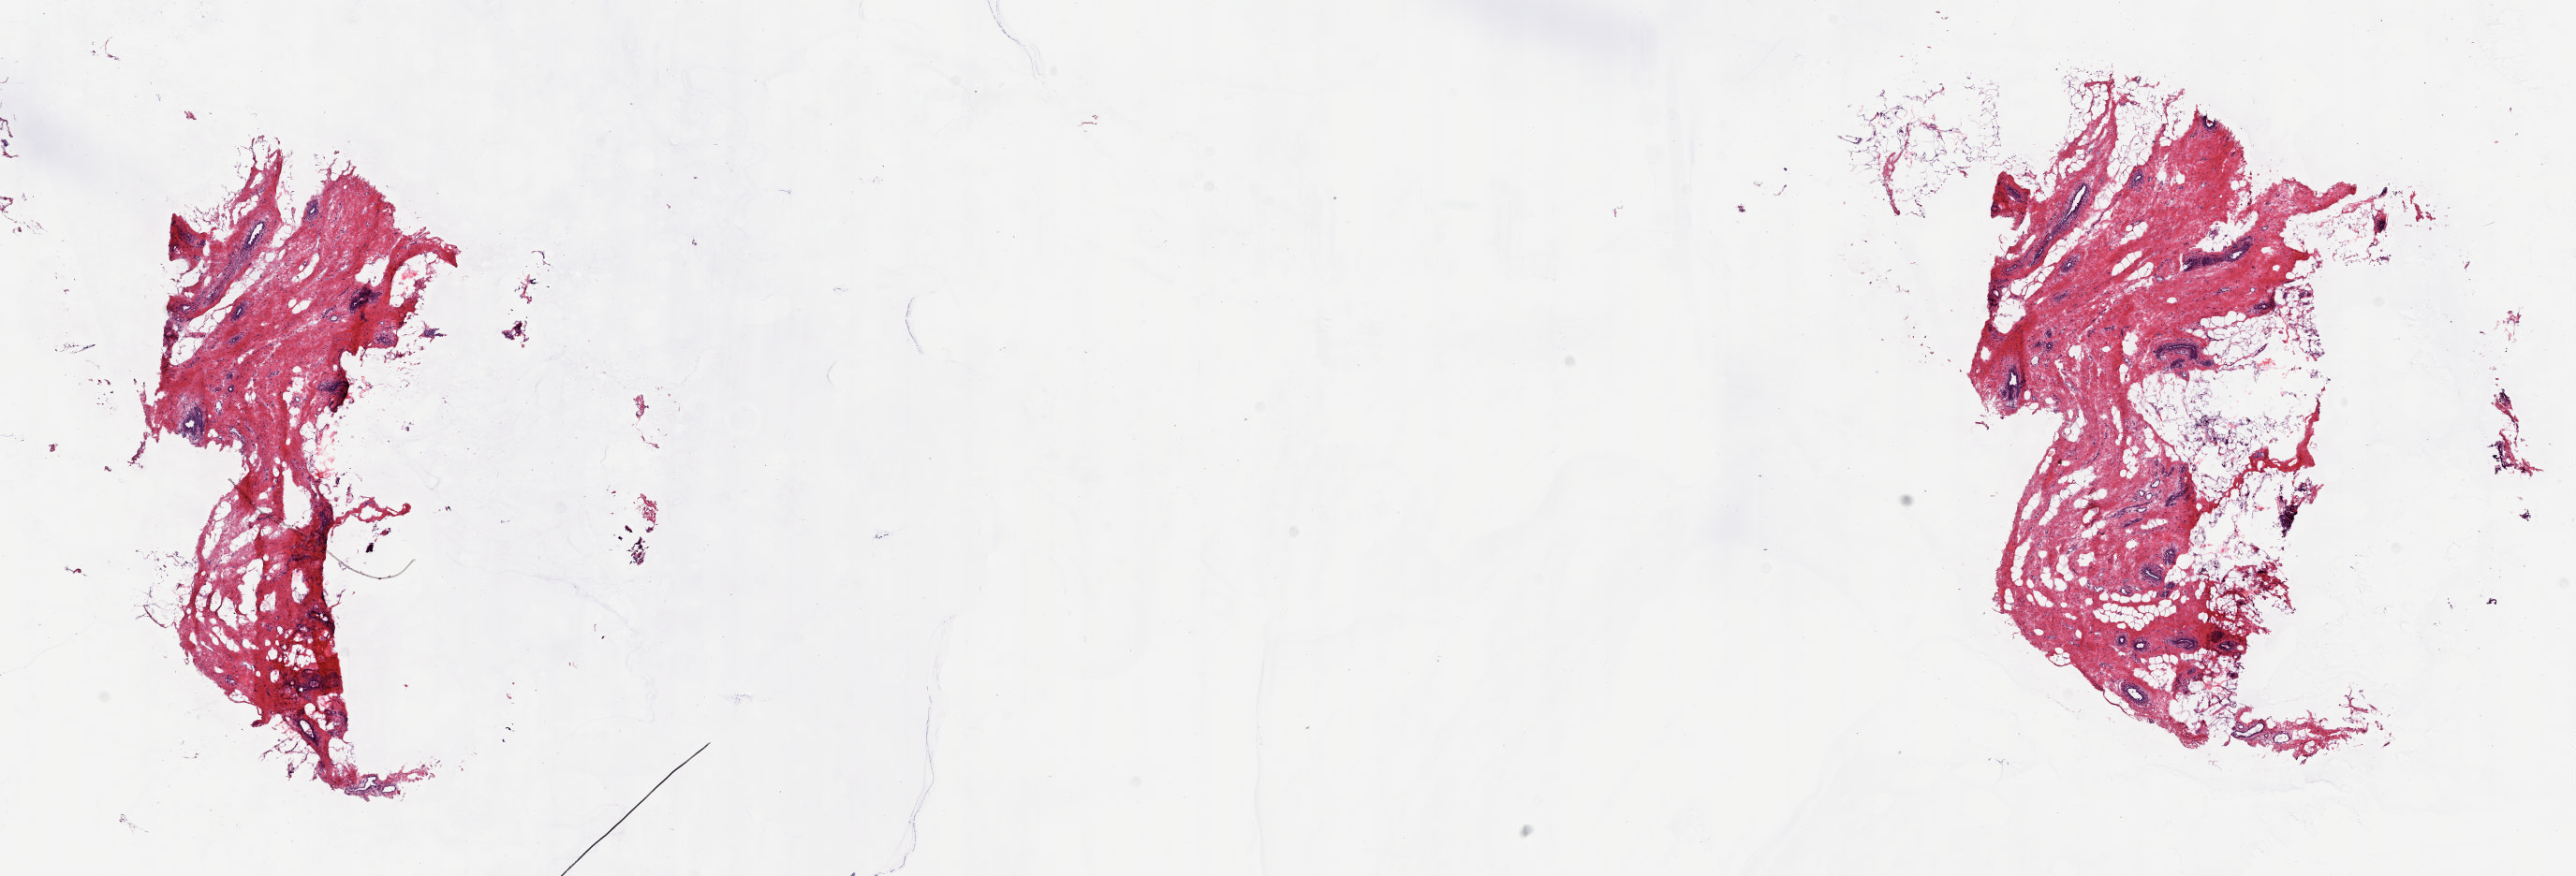
Digitized H&E tissue section (whole slide) — shown as a low-resolution overview of the whole scanned area (about 21.8 x 7.4 mm); frozen section; solid tissue normal (non-tumour tissue) sample from the breast. Patient: female, age at initial diagnosis 62 years. Composition of this section per pathologist review: tumour cells 0%, tumour nuclei 0%, normal cells 100%, stromal cells 0%, necrosis 0%. Inflammatory infiltration, as recorded: lymphocyte infiltration 1%, monocyte infiltration 0%, neutrophil infiltration 0%.
This section: solid tissue normal (non-tumour) sample from the same patient. Patient diagnosis: Lobular carcinoma, NOS.